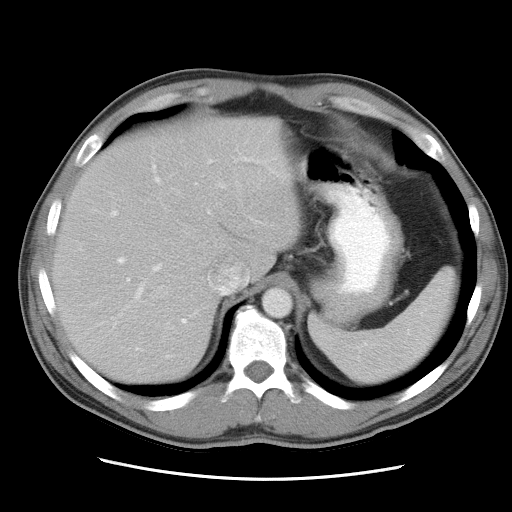
Contrast-enhanced abdominal CT, one axial slice; slice 23 of 34 in the series (ordered by position); 120 kVp; intravenous contrast given; soft-tissue window (W 400 / L 40 HU); 7.5 mm slice thickness; 512 × 512 image matrix, field of view 360 × 360 mm. Male patient, age 40 years. Case-level facts recorded for this patient, not image findings: diagnosis: colorectal cancer liver metastases, imaged before liver resection; multiple liver metastases: yes; largest metastasis: 1.5 cm; chemotherapy before resection: no.
Outlined on this slice (expert manual segmentation):
- hepatic veins: bounding box (x1, y1, x2, y2) in pixels: (150, 267, 249, 300)
- liver: (55, 117, 301, 384)
- planned liver remnant (the part of the liver to remain after resection): (55, 117, 302, 383)
- portal vein (with intrahepatic branches): (110, 157, 253, 324)